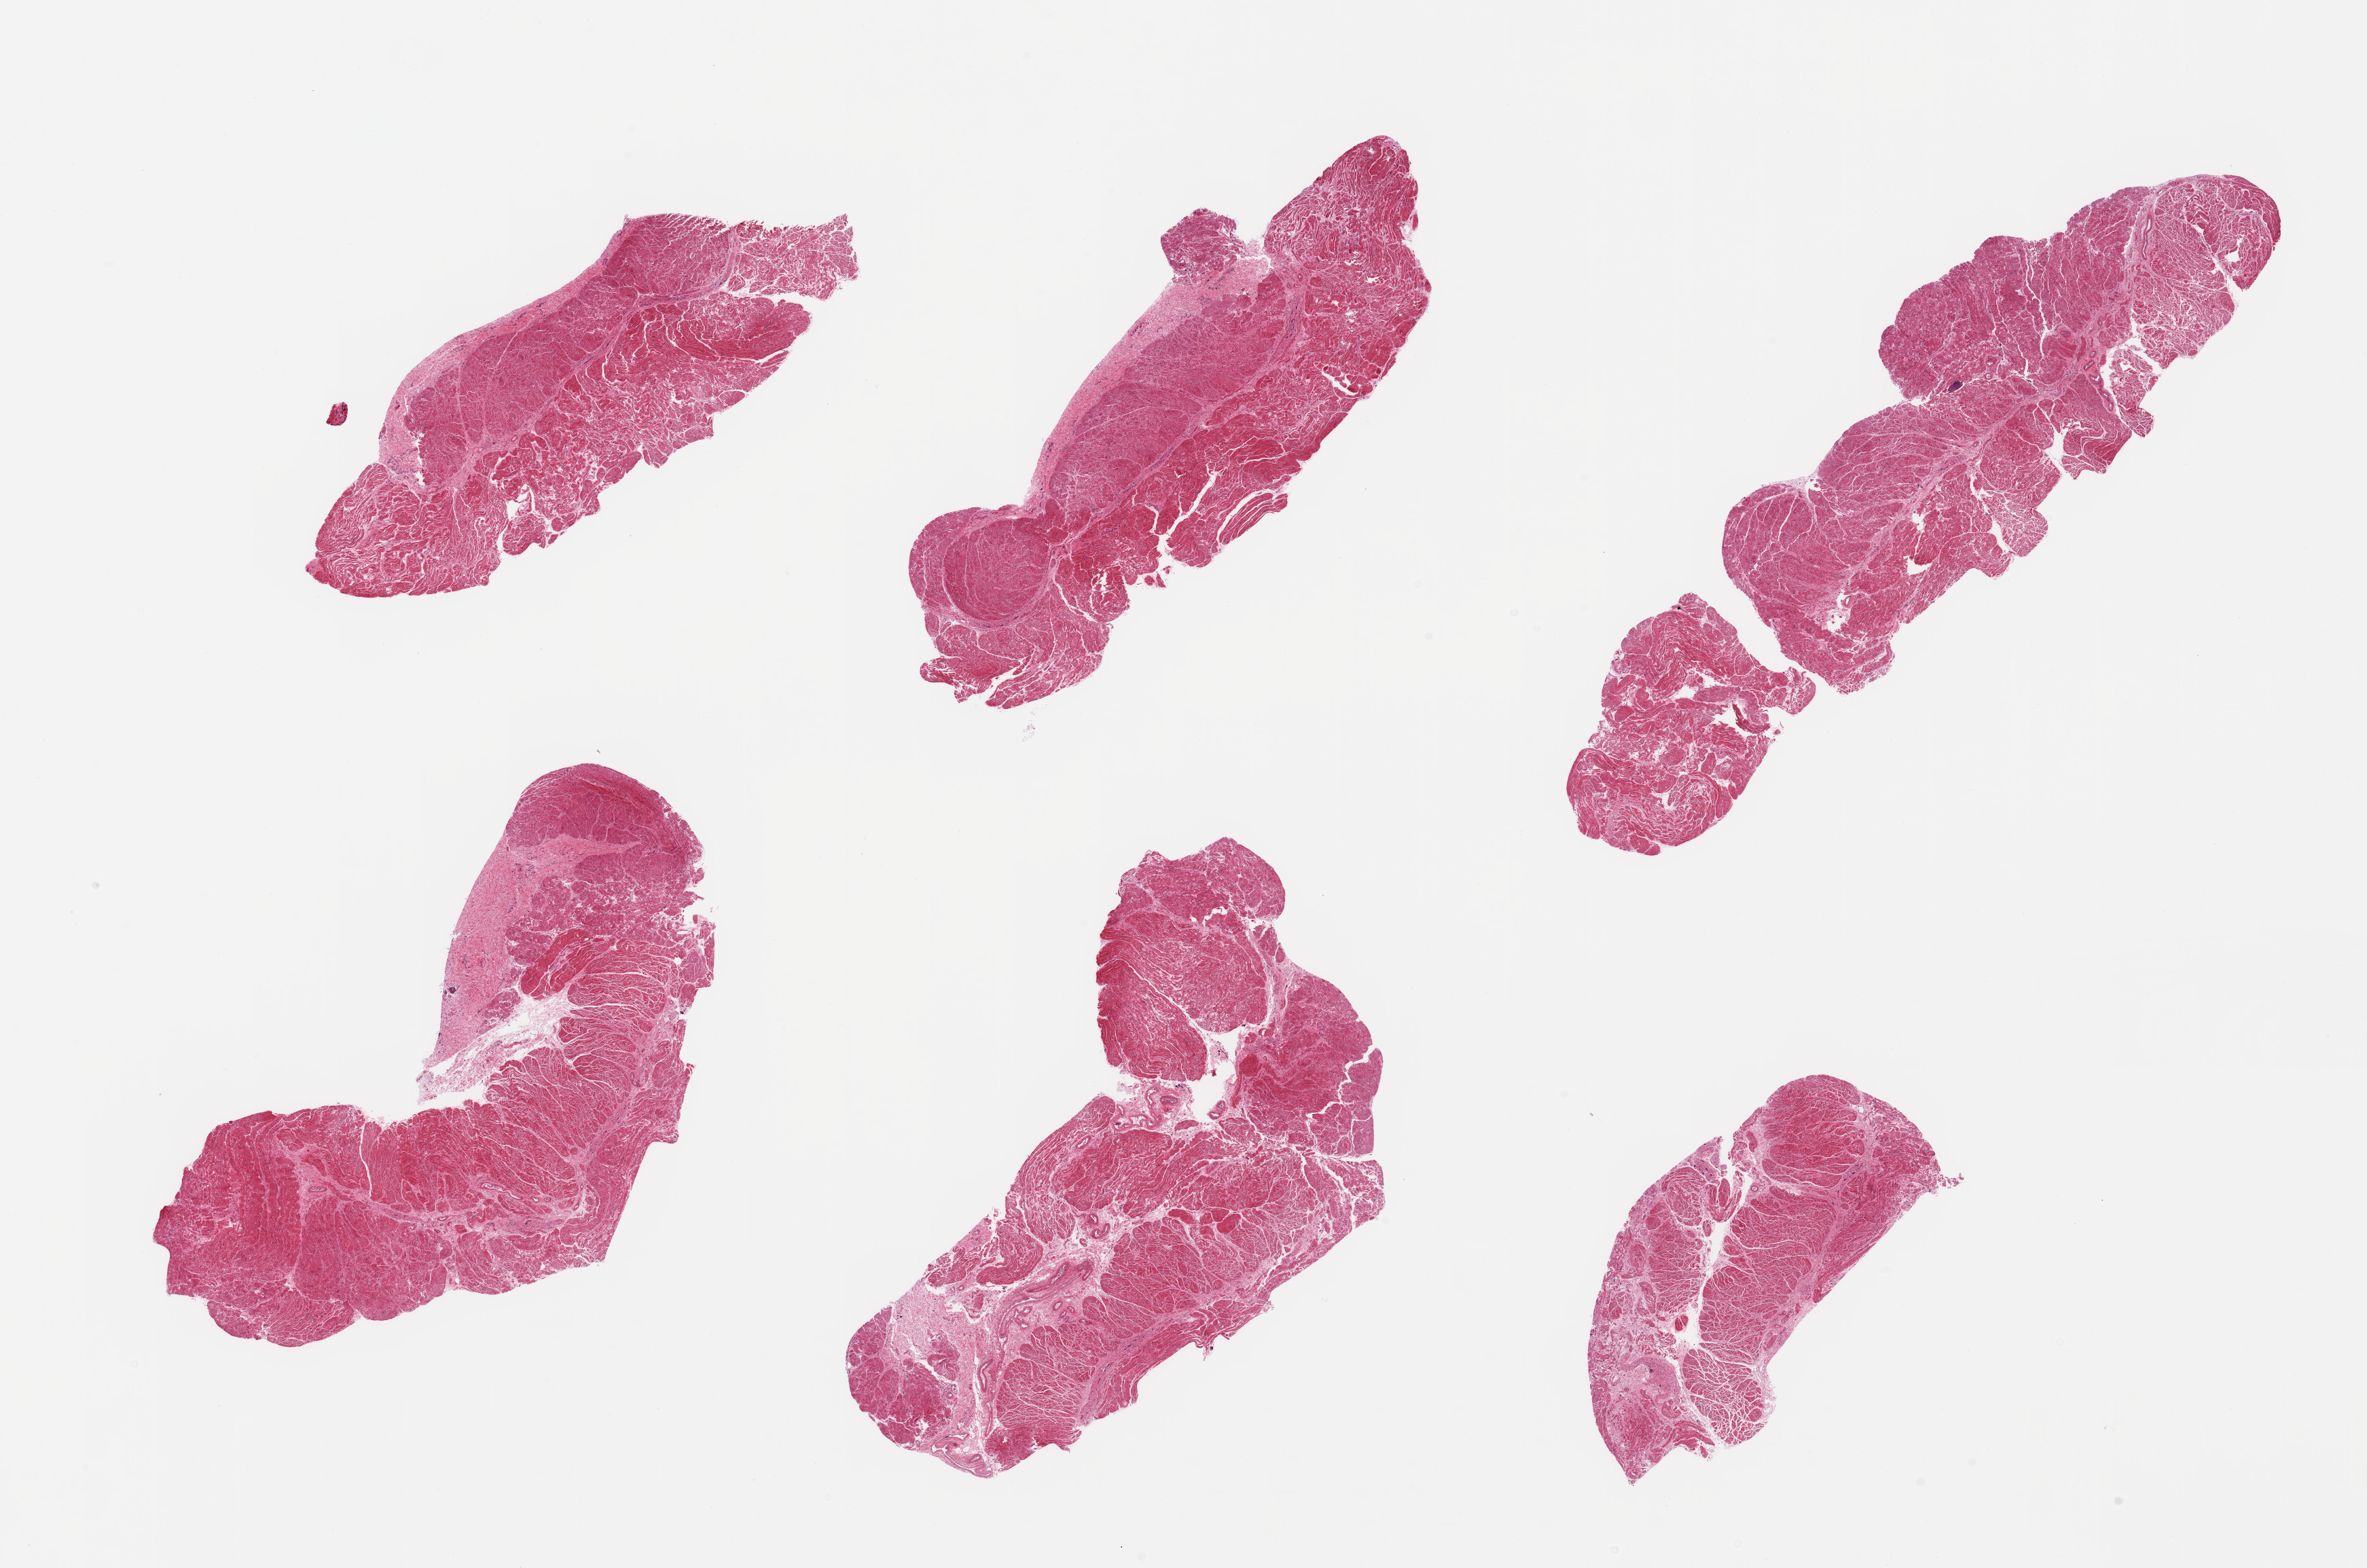
Haematoxylin and eosin whole-slide image, a low-resolution overview of the entire scanned area, about 27.6 x 18.3 mm (acquisition: 20x scan). PAXgene-fixed, paraffin-embedded tissue. Section of gastroesophageal junction (target tissue). Donor tissue sample. Male donor.
• reviewer comment on this tissue sample: 6 pieces; up to 10% fibrous content